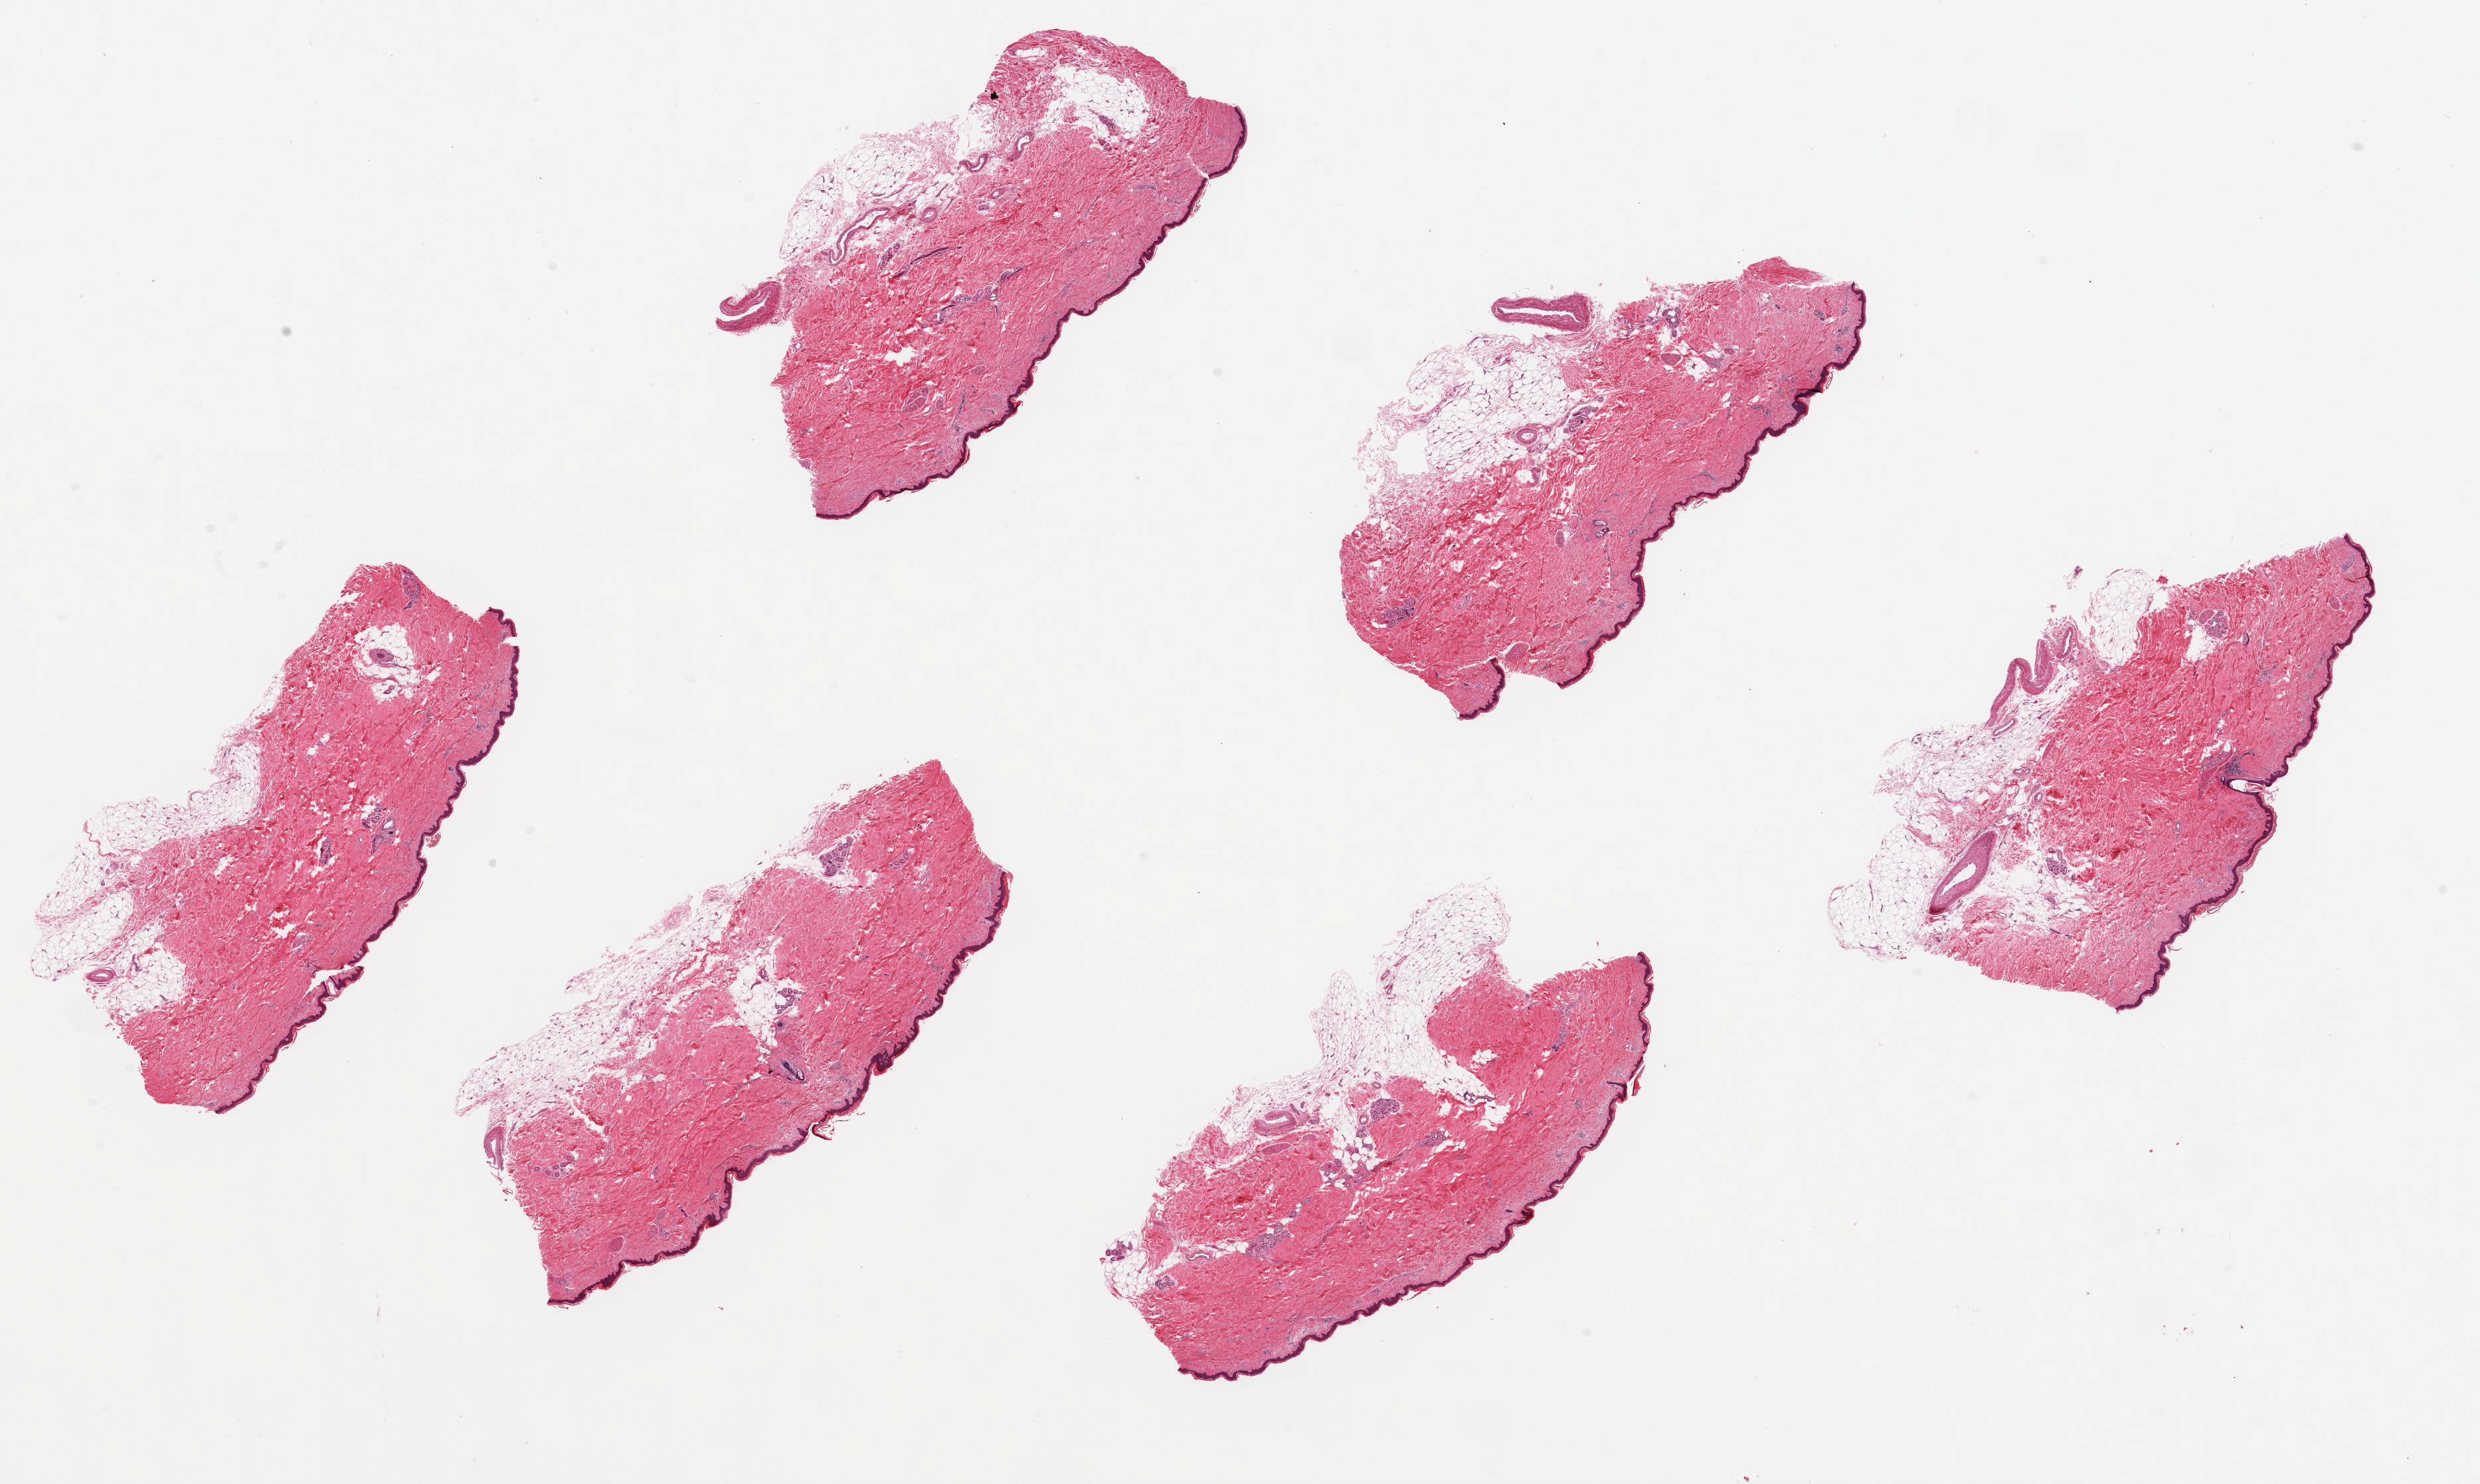
Digitized haematoxylin and eosin-stained section — a low-resolution overview of the entire scanned area, about 29.5 x 17.7 mm (slide scanned at 20x); PAXgene-fixed, paraffin-embedded tissue; section of skin of lower leg (target tissue); donor tissue sample. Donor sex: male.
Pathologist's review note for this sample: 6 pieces, ~7x2.5mm. Squamous epithelium is ~1-2% of thickness.